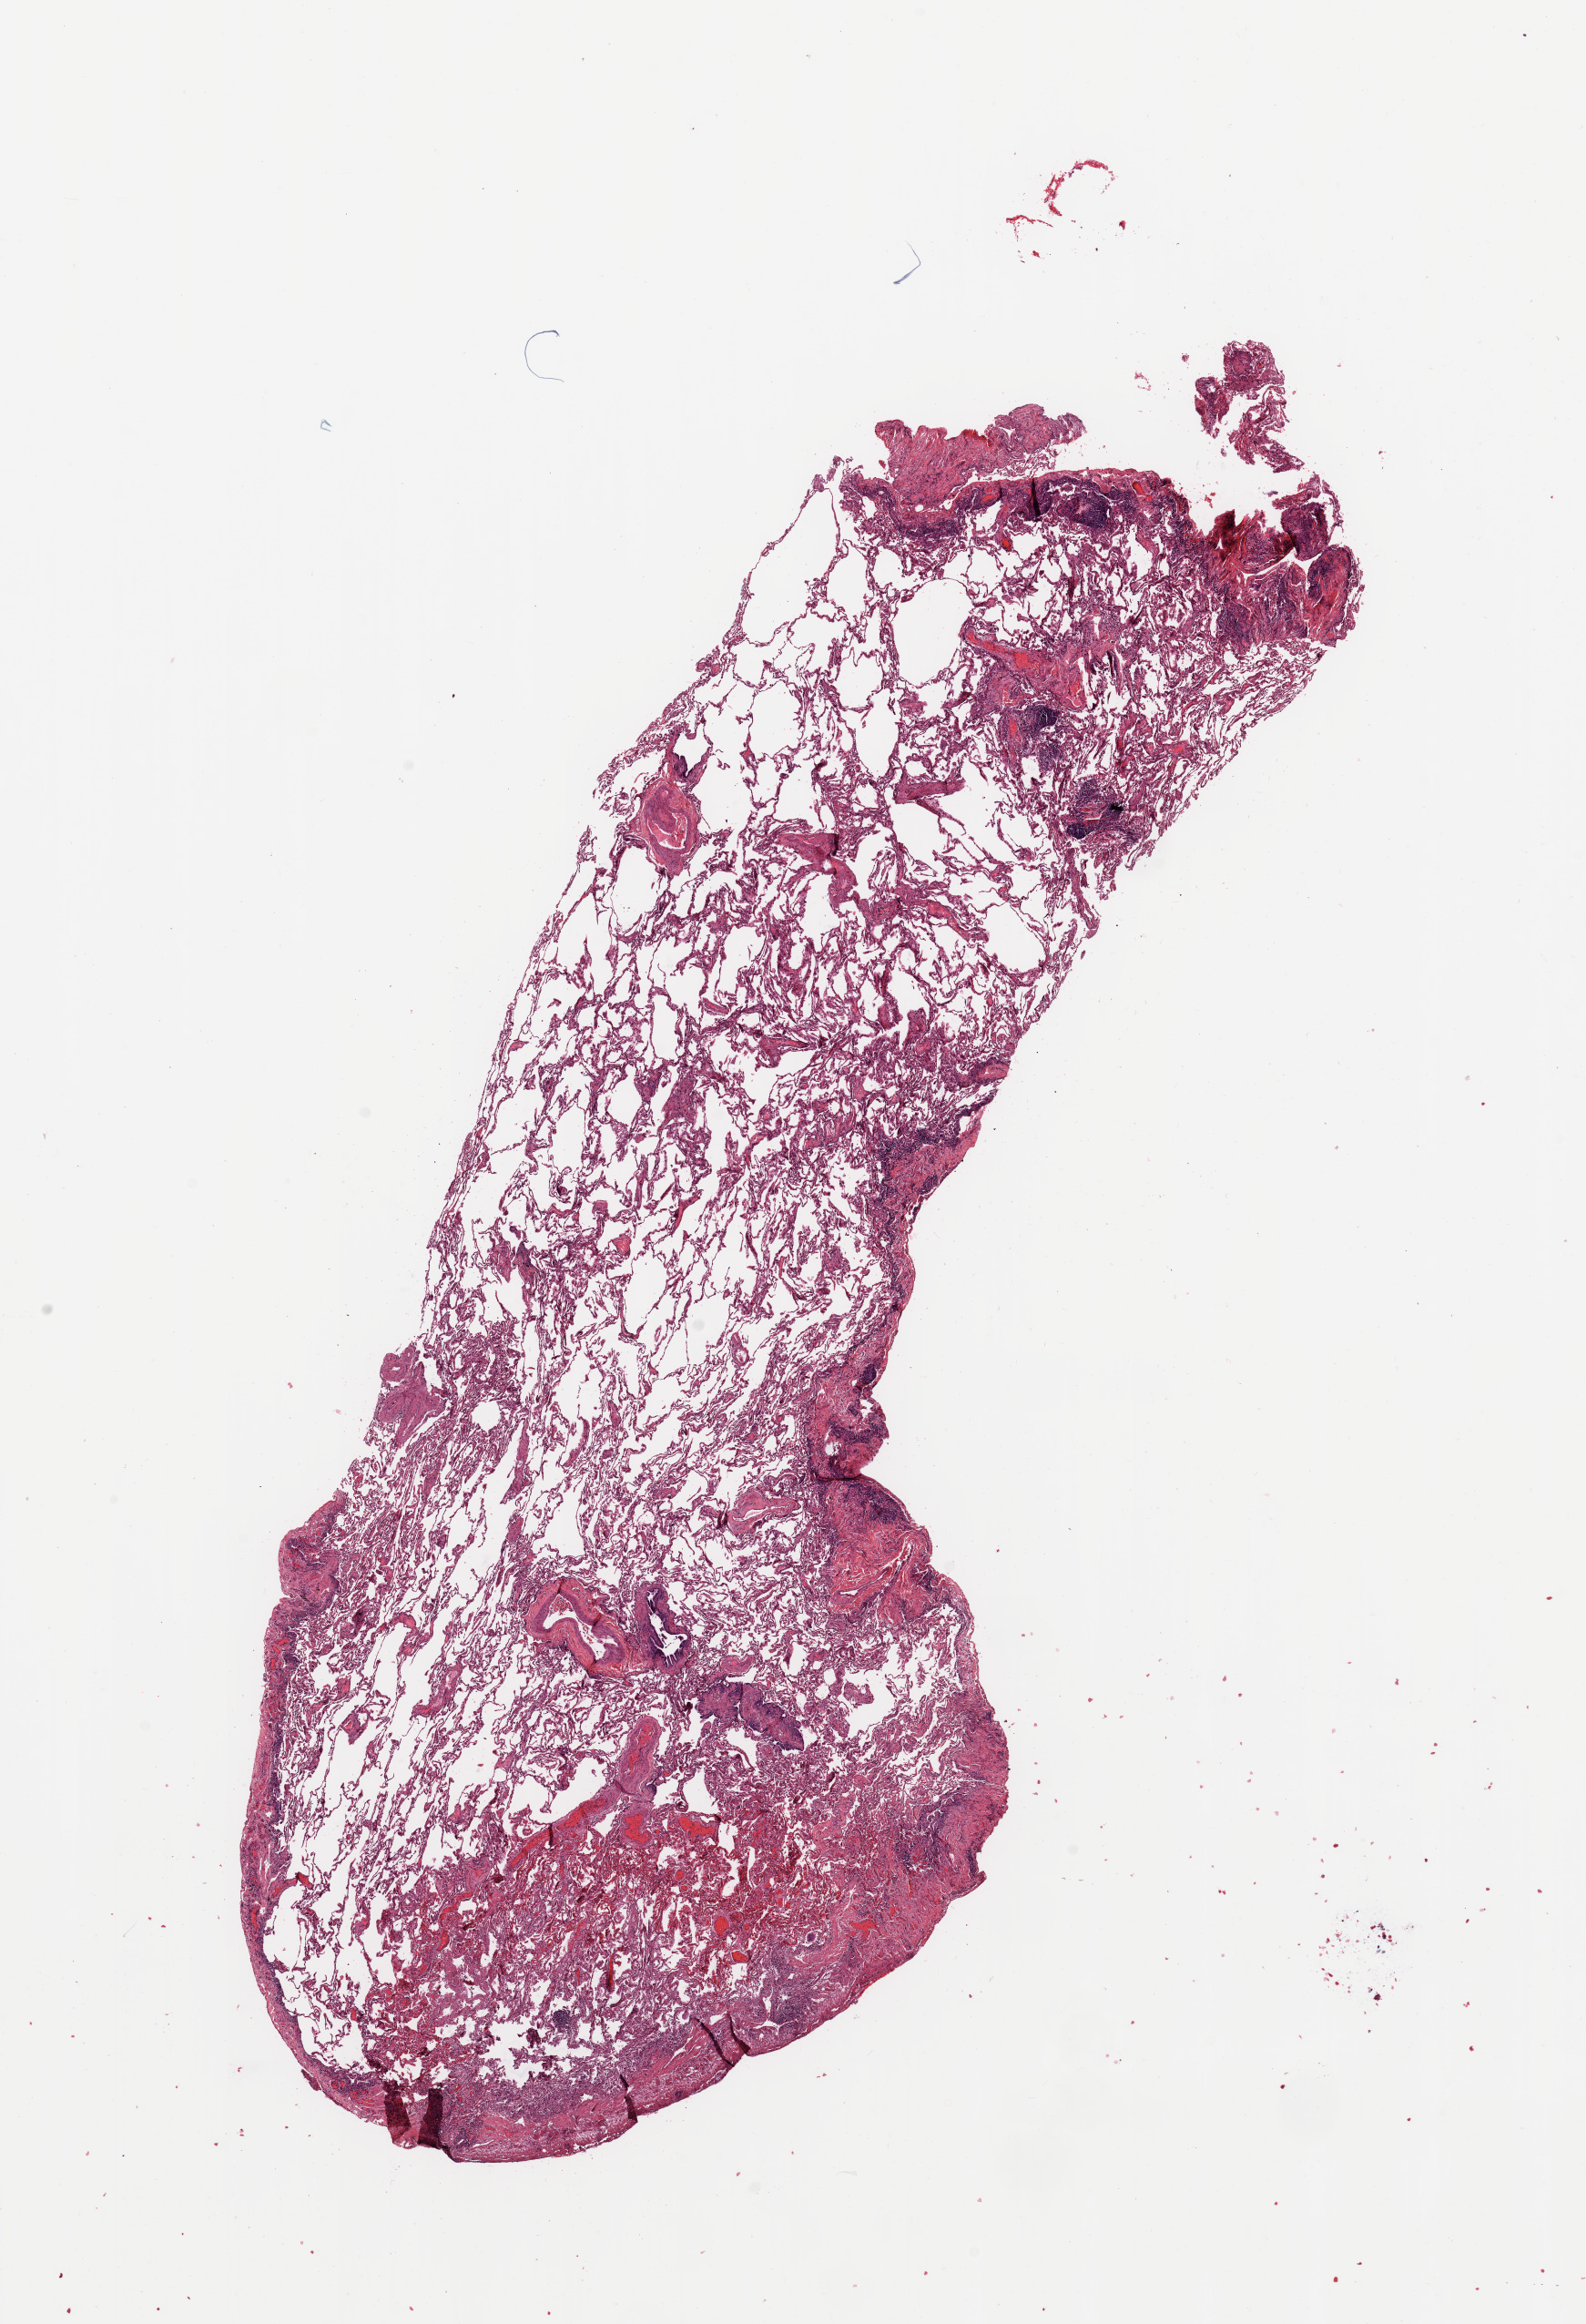
Whole-slide histology image, Hematoxylin and eosin (H&E) stained, whole scanned area (about 13.8 x 20.2 mm) shown as a low-resolution overview; normal (non-tumour) tissue sample, lung. Male, 88 y/o.
This section: normal (non-tumour) tissue from the same patient. Patient diagnosis: Squamous cell carcinoma, NOS.